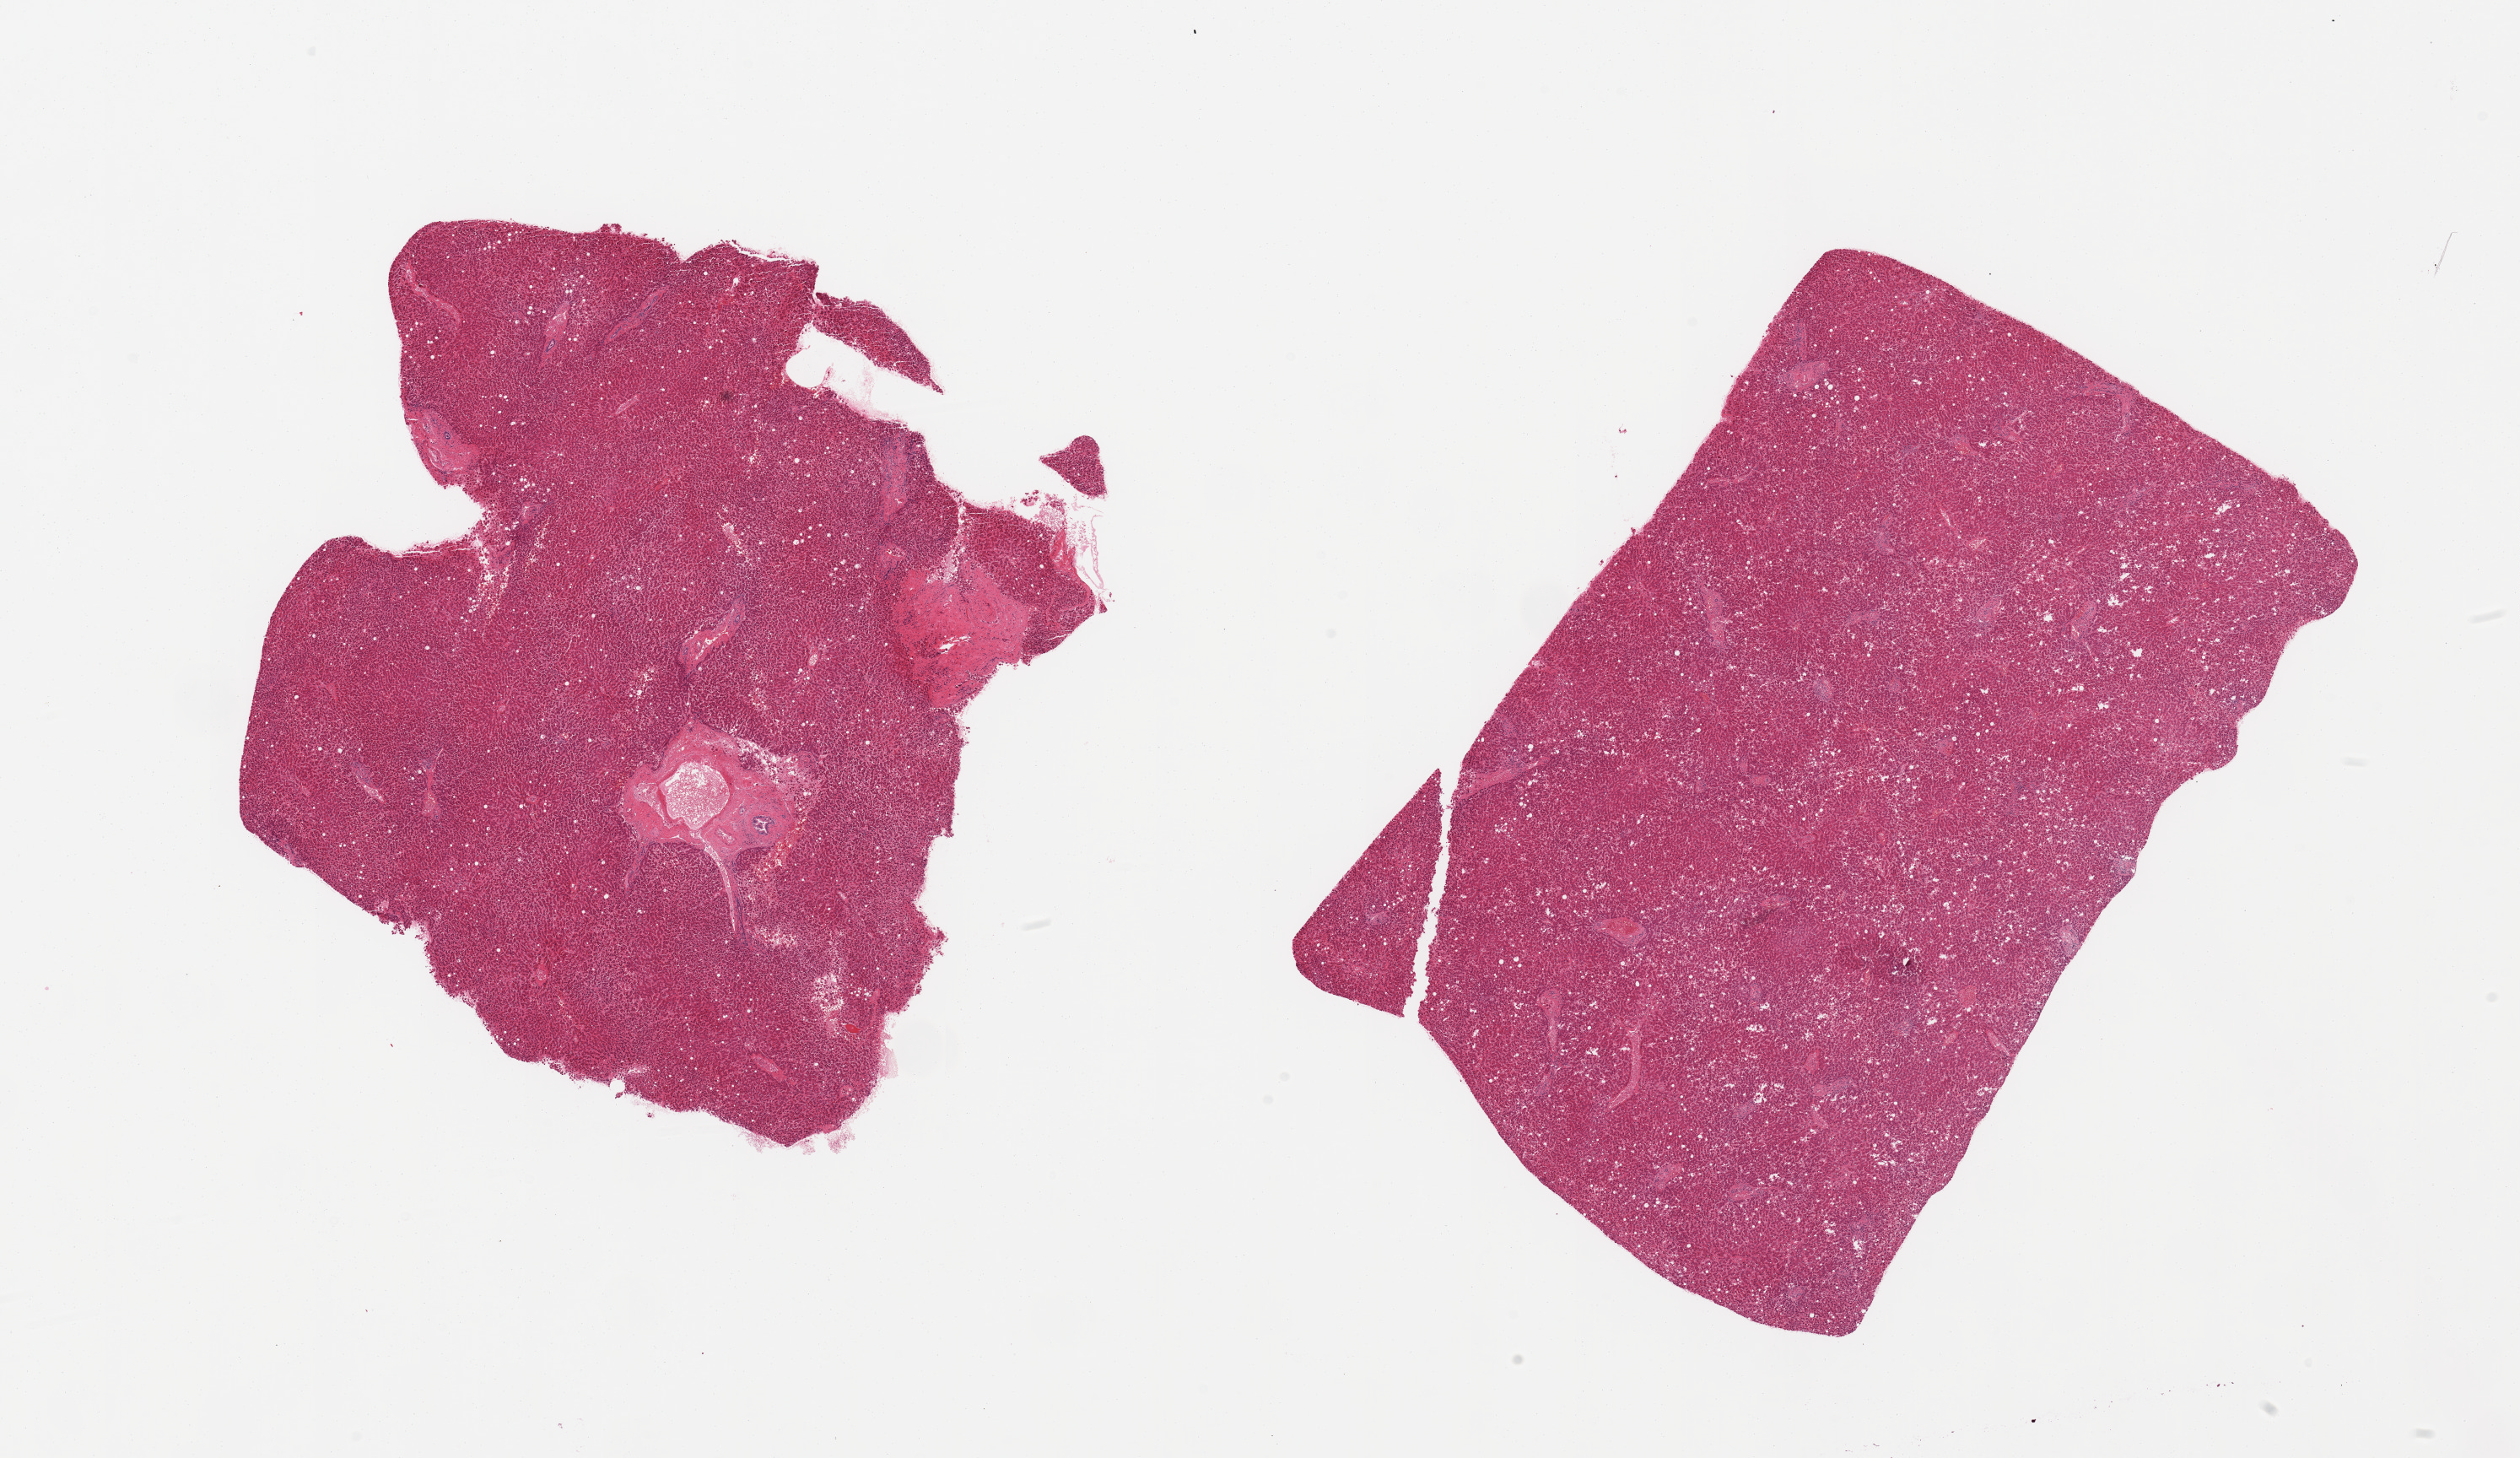
Hematoxylin and eosin (H&E) whole-slide image, shown as a low-resolution overview of the whole scanned area (about 23.6 x 13.7 mm), PAXgene-fixed, paraffin-embedded tissue, sampled site (target tissue): liver, tissue donor sample. Male donor.
Pathologist's review note for this sample: 2 pieces, macrovesicular steatosis in ~25% of parenchyma, mild/moderate passive congestion.